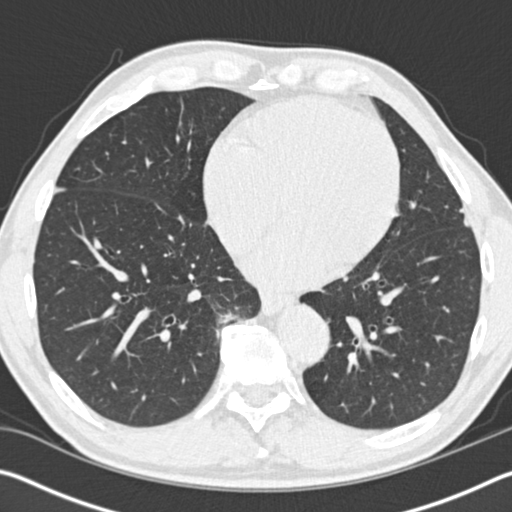
Low-dose screening chest CT, one axial slice; slice 55 of 162 in the series (ordered by position); reconstruction kernel B30f; 120 kVp; lung window (W 1500 / L -600 HU); 2 mm slice thickness; 512 × 512 image matrix, field of view 340 × 340 mm.
Outlined on this slice (outlined manually by an expert reader):
- lesion 1 (tumor, upper lobe of left lung): bounding box <459,209,470,227> (left, top, right, bottom; pixels)